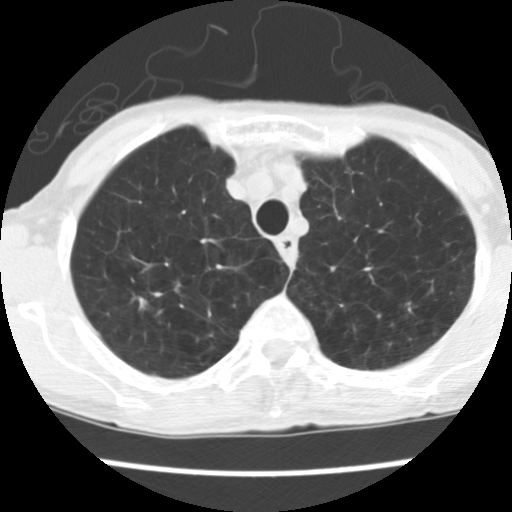
Chest CT (low-dose screening protocol), one axial image. Baseline annual screen. Lung window (W 1500 / L -600 HU). Slice 28 of 160 in the series. 512 × 512 image matrix. Female, age 70 years at enrolment. Former smoker at enrolment.
Expert-annotated lung lesion, box from (x=116, y=280) to (x=169, y=335) px. Screening reader's record for this exam: no non-calcified nodule ≥4 mm recorded. Official screen result: negative screen, significant abnormalities not suspicious for lung cancer. Participant outcome: lung cancer diagnosed 226 days after this screen — large cell neuroendocrine carcinoma, right upper lobe, stage IA (AJCC 6th edition), 30 mm at pathology.